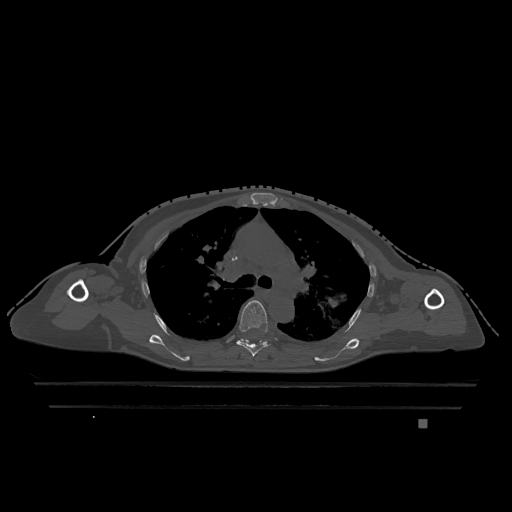
CT including the spine, one axial slice. Slice 830 of 1317 in the series (ordered by position). Bone window (W 1800 / L 400 HU). 0.5 mm slice thickness. 512 × 512 image matrix. Female patient, age 74 years. From the clinical record (not read from this slice): primary cancer: lung.
Structures marked on this image (semi-automatically segmented with operator editing):
- T5 vertebra: box from (x=236, y=300) to (x=269, y=357) px
- T6 vertebra: (x=240, y=339)–(x=244, y=342)